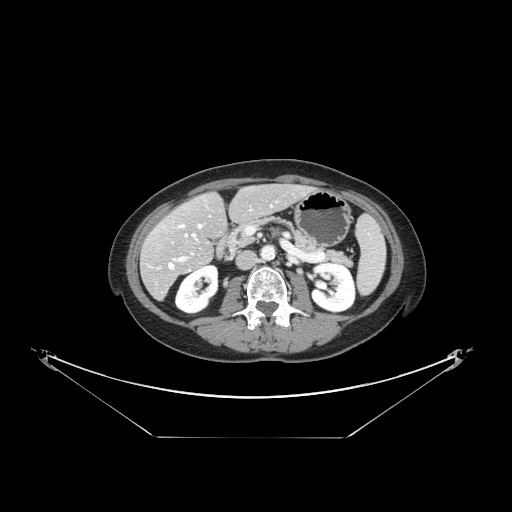
Contrast-enhanced abdominal CT, one axial slice. Slice 60 of 148 in the series (ordered by position). Reconstruction kernel STANDARD. 120 kVp. Intravenous contrast given. Soft-tissue window (W 400 / L 40 HU). 2.5 mm slice thickness. 512 × 512 image matrix, field of view 500 × 500 mm. Female patient, age 73 years. Case-level facts recorded for this patient, not image findings: diagnosis: colorectal cancer liver metastases, imaged before liver resection; multiple liver metastases: no; largest metastasis: 1 cm; disease in both lobes: no.
Outlined on this slice (outlined manually by an expert reader):
- hepatic veins: bounding box <169,205,272,268> (left, top, right, bottom; pixels)
- liver: <142,185,309,298>
- planned liver remnant (the part of the liver to remain after resection): <165,185,308,250>
- portal vein (with intrahepatic branches): <174,258,185,261>